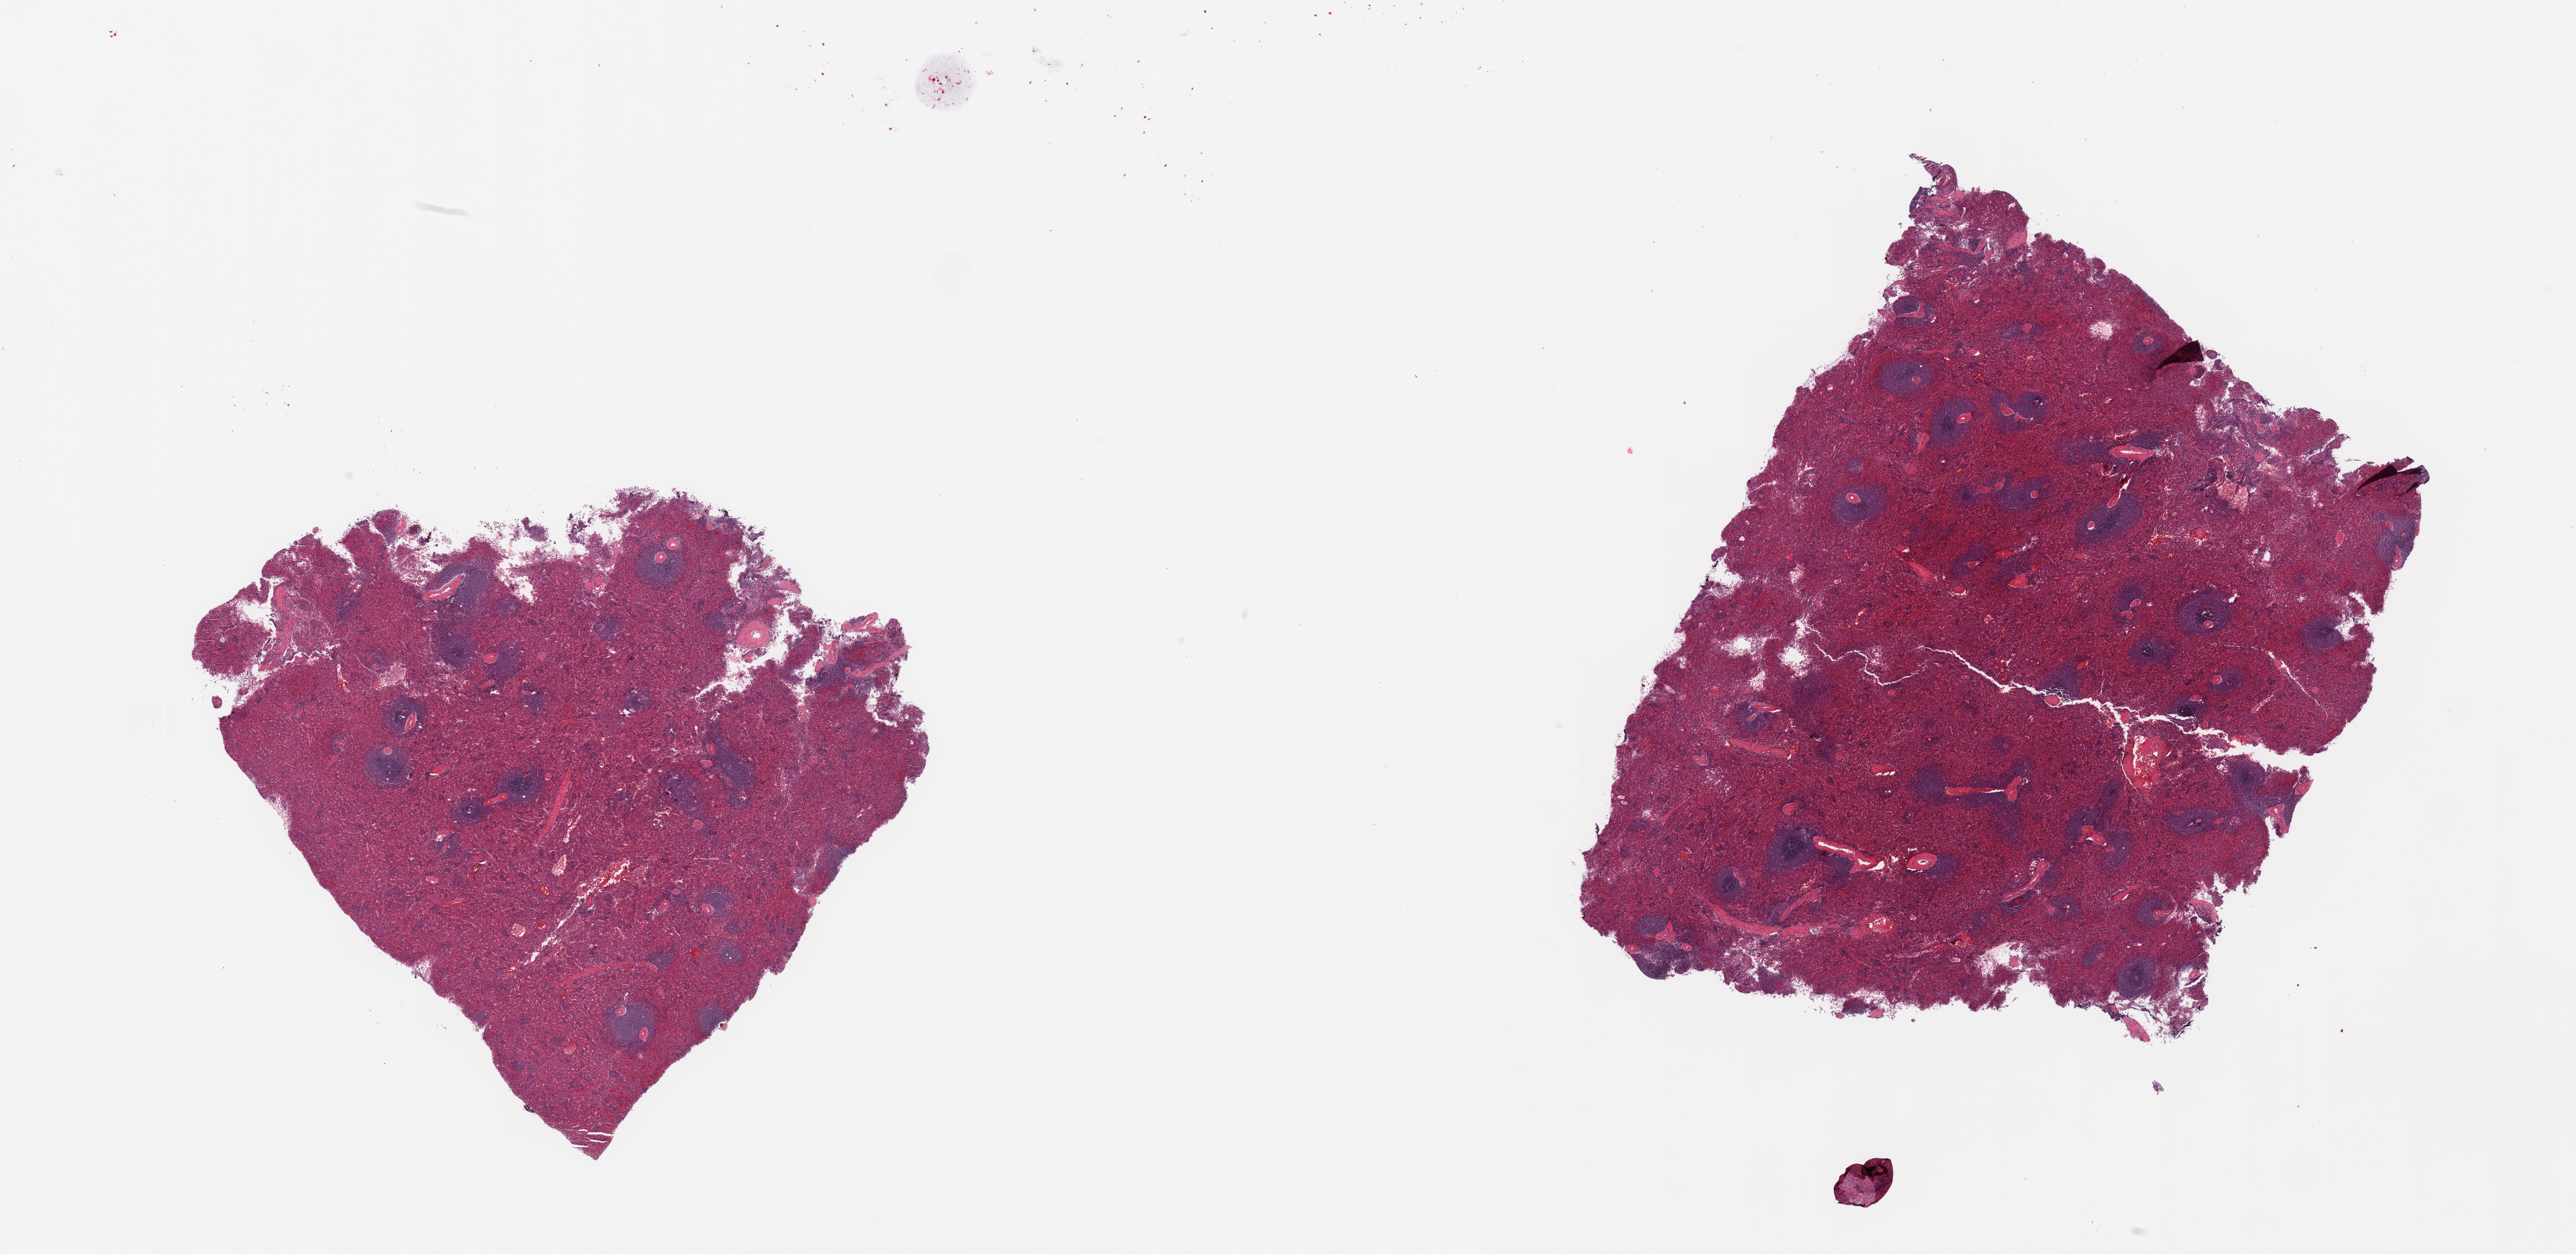
Digitized hematoxylin and eosin (H&E)-stained section, brightfield — a low-resolution overview of the entire scanned area, about 30.5 x 14.9 mm (slide scanned at 20x), PAXgene-fixed, paraffin-embedded tissue, sampled site (target tissue): spleen, tissue donor sample. Female donor.
• review note (as recorded): 2 partly fragmented pieces; slight congestion